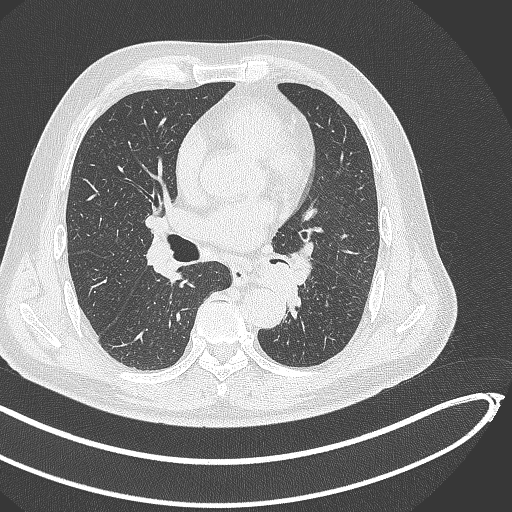
Chest CT, one axial slice; slice 248 of 468 in the series (ordered by position); reconstruction kernel B70f; lung window (W 1500 / L -600 HU); 512 × 512 image matrix. Patient: male, 64 years. Case-level facts recorded for this patient, not image findings: clinical TNM (as recorded): T1c N0 M0; histopathological grade: G2.
Outlined on this slice (rectangle marked by the reading radiologist):
- lung tumour (recorded histology: squamous cell carcinoma): bounding box <257,256,301,318> (left, top, right, bottom; pixels)